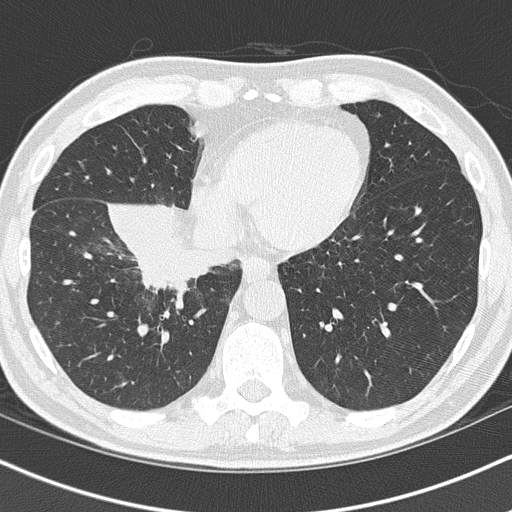
Chest CT (low-dose screening protocol), one axial image, baseline annual screen, lung window (W 1500 / L -600 HU), 2 mm slice thickness, slice 38 of 151 in the series, 512 × 512 image matrix, field of view 320 × 320 mm. Male, age 55 years at enrolment.
Expert reader's lesion annotation, box from (x=118, y=221) to (x=244, y=317) px. The exam's reader record, not a measurement of the box and not confirmed to be the same lesion: non-calcified nodule or mass ≥4 mm, right lower lobe, 6 × 5 mm, spiculated (stellate) margins, soft tissue attenuation. Lung cancer was diagnosed 21 days after this screen: carcinoma, NOS, right hilum, stage IB (AJCC 6th edition), 67 mm at pathology.